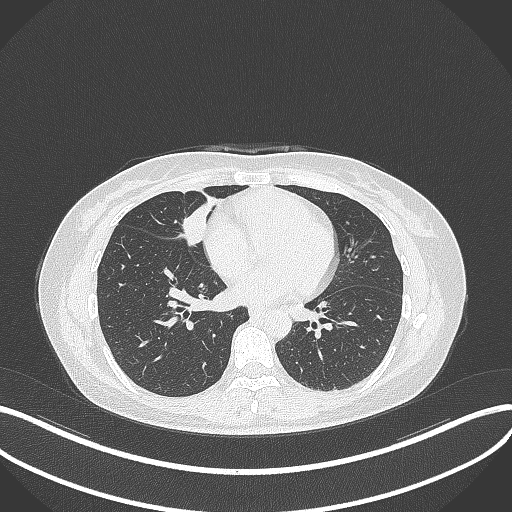
Chest CT, one axial slice; position 118 of 284 along the scan axis; reconstruction kernel B70f; lung window (W 1500 / L -600 HU); 1 mm slice thickness; 512 × 512 image matrix, field of view 400 × 400 mm. Patient: female, 43 years. From the clinical record (not read from this slice): clinical TNM (as recorded): T1c N3 M1; histopathological grade: G1.
Annotated regions visible in this slice (rectangle marked by the reading radiologist):
- lung tumour (recorded histology: adenocarcinoma): box from (x=179, y=200) to (x=209, y=252) px